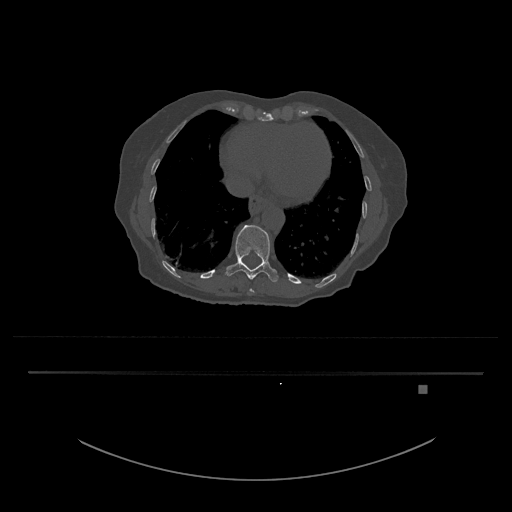
CT including the spine, one axial slice. Position 669 of 797 along the scan axis. 120 kVp. Bone window (W 1800 / L 400 HU). 512 × 512 image matrix, field of view 500 × 500 mm. Patient: female, 57 years. From the clinical record (not read from this slice): primary cancer: cervical.
Outlined on this slice (semi-automatically segmented with operator editing):
- T10 vertebra: box from (x=250, y=289) to (x=254, y=293) px
- T11 vertebra: (x=226, y=225)–(x=279, y=282)